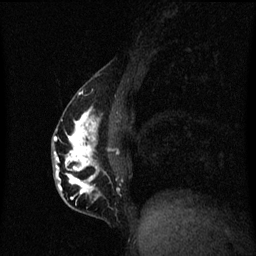
Breast MRI (dynamic contrast-enhanced), one sagittal slice; position 23 of 60 along the scan axis; dynamic contrast-enhanced series, image 2 of 3 at this slice position (ordered by acquisition); 1.5 T; TE 4.2 ms, TR 8.4 ms; 256 × 256 image matrix, field of view 200 × 200 mm. Female patient, age 40 years.
Annotated regions visible in this slice (semi-automatic segmentation, software-assisted and operator-edited):
- analysis volume of interest (the breast-tissue region the enhancement analysis was run in; not a lesion): box from (x=53, y=84) to (x=116, y=211) px
- tumour enhancement mask (voxels above the 70 % enhancement threshold inside the analysis volume of interest): (x=54, y=106)–(x=101, y=201)